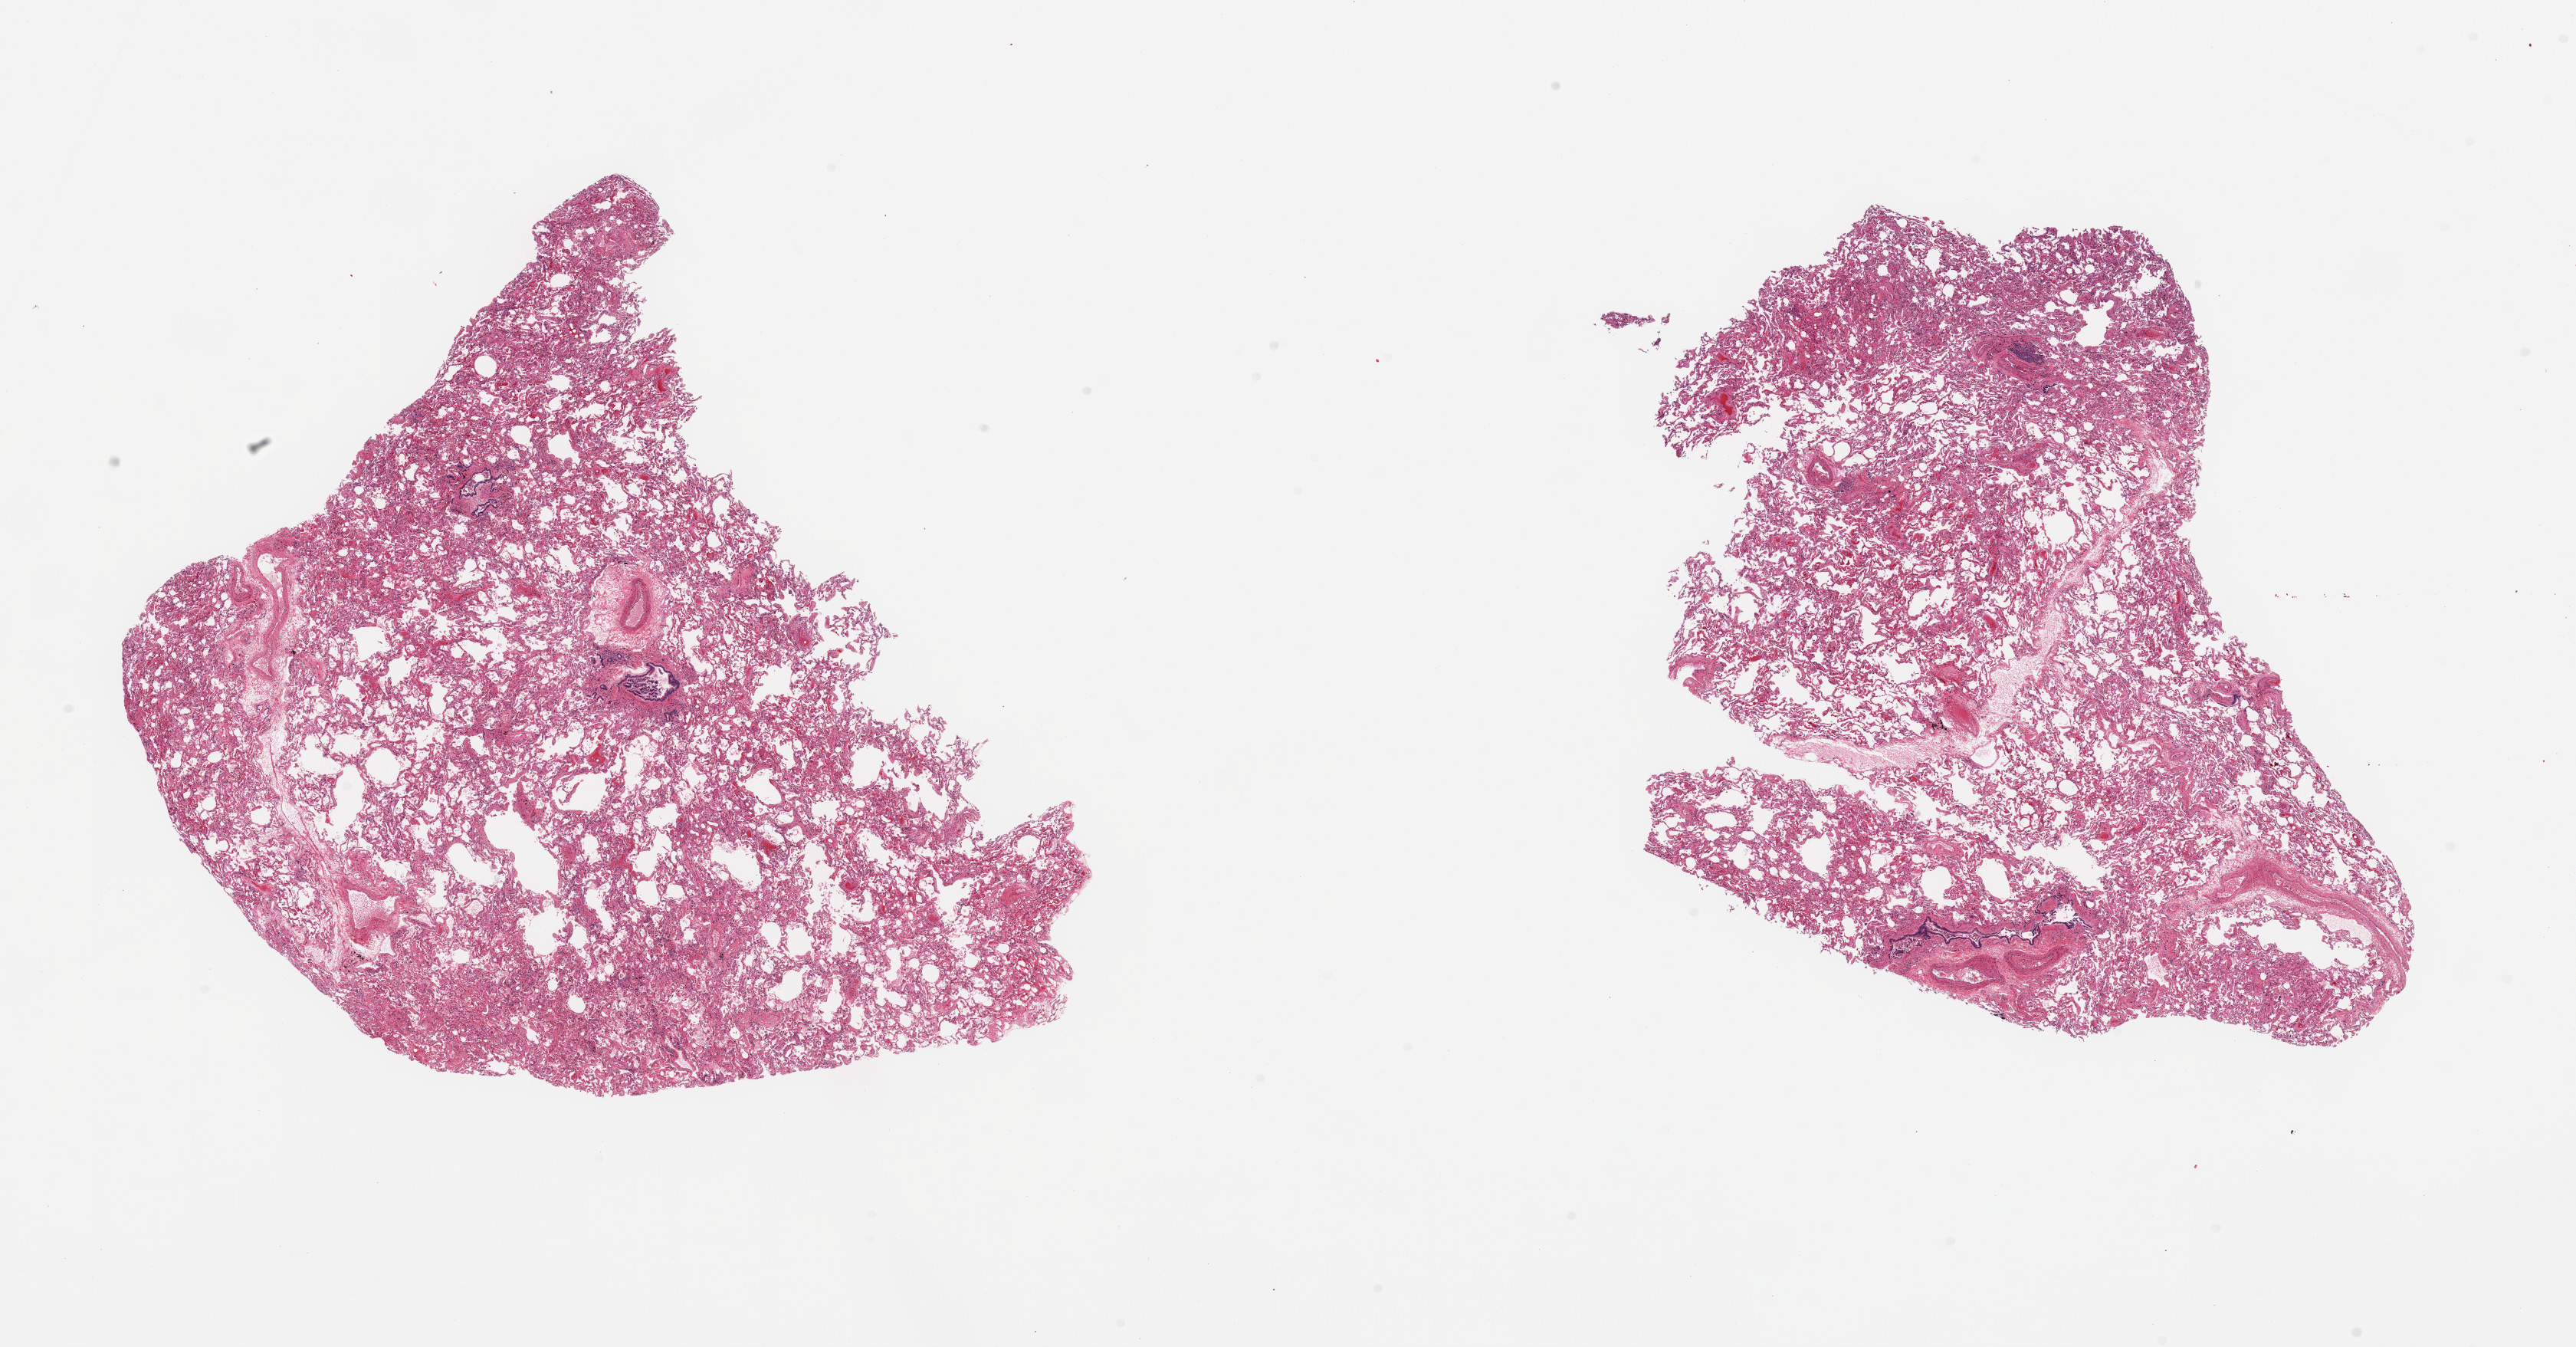
Whole-slide image, haematoxylin and eosin stain, brightfield, whole scanned area (about 26.6 x 13.9 mm) shown as a low-resolution overview; PAXgene-fixed, paraffin-embedded tissue; target tissue: lung; tissue donor sample. Donor sex: male.
Pathologist's review note for this sample: 2 pieces; mild emphysema.